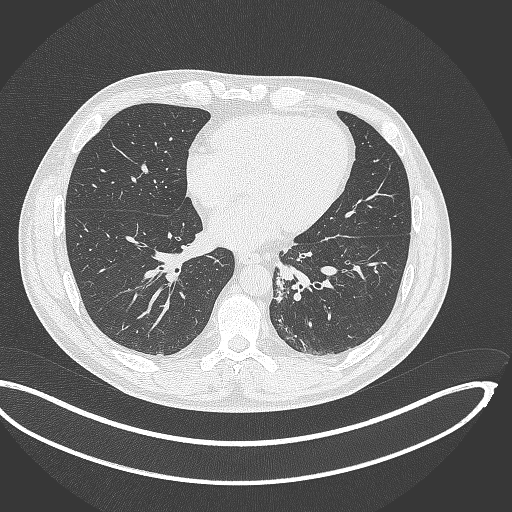
Chest CT, one axial slice. Slice 134 of 362 in the series (ordered by position). Lung window (W 1500 / L -600 HU). 1 mm slice thickness. 512 × 512 image matrix. Male patient, age 50 years. From the clinical record (not read from this slice): clinical TNM (as recorded): T2a N3 M0.
Annotated regions visible in this slice (rectangle marked by the reading radiologist):
- lung tumour (recorded histology: squamous cell carcinoma): bounding box (x1, y1, x2, y2) in pixels: (274, 272, 288, 304)